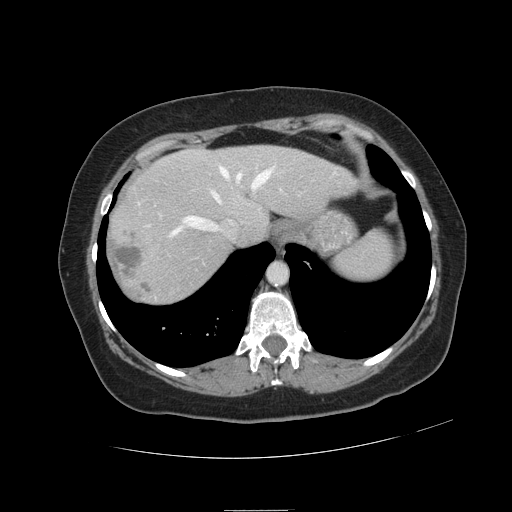
Contrast-enhanced abdominal CT, one axial slice; position 97 of 121 along the scan axis; 120 kVp; intravenous contrast given; soft-tissue window (W 400 / L 40 HU); 512 × 512 image matrix, field of view 400 × 400 mm. Female patient, age 52 years. From the clinical record (not read from this slice): diagnosis: colorectal cancer liver metastases, imaged before liver resection.
Structures marked on this image (manually delineated by an expert):
- hepatic veins: bounding box (x1, y1, x2, y2) in pixels: (138, 166, 275, 236)
- liver: (107, 146, 352, 305)
- planned liver remnant (the part of the liver to remain after resection): (169, 146, 352, 243)
- portal vein (with intrahepatic branches): (280, 189, 282, 191)
- liver metastasis: (111, 246, 141, 280)